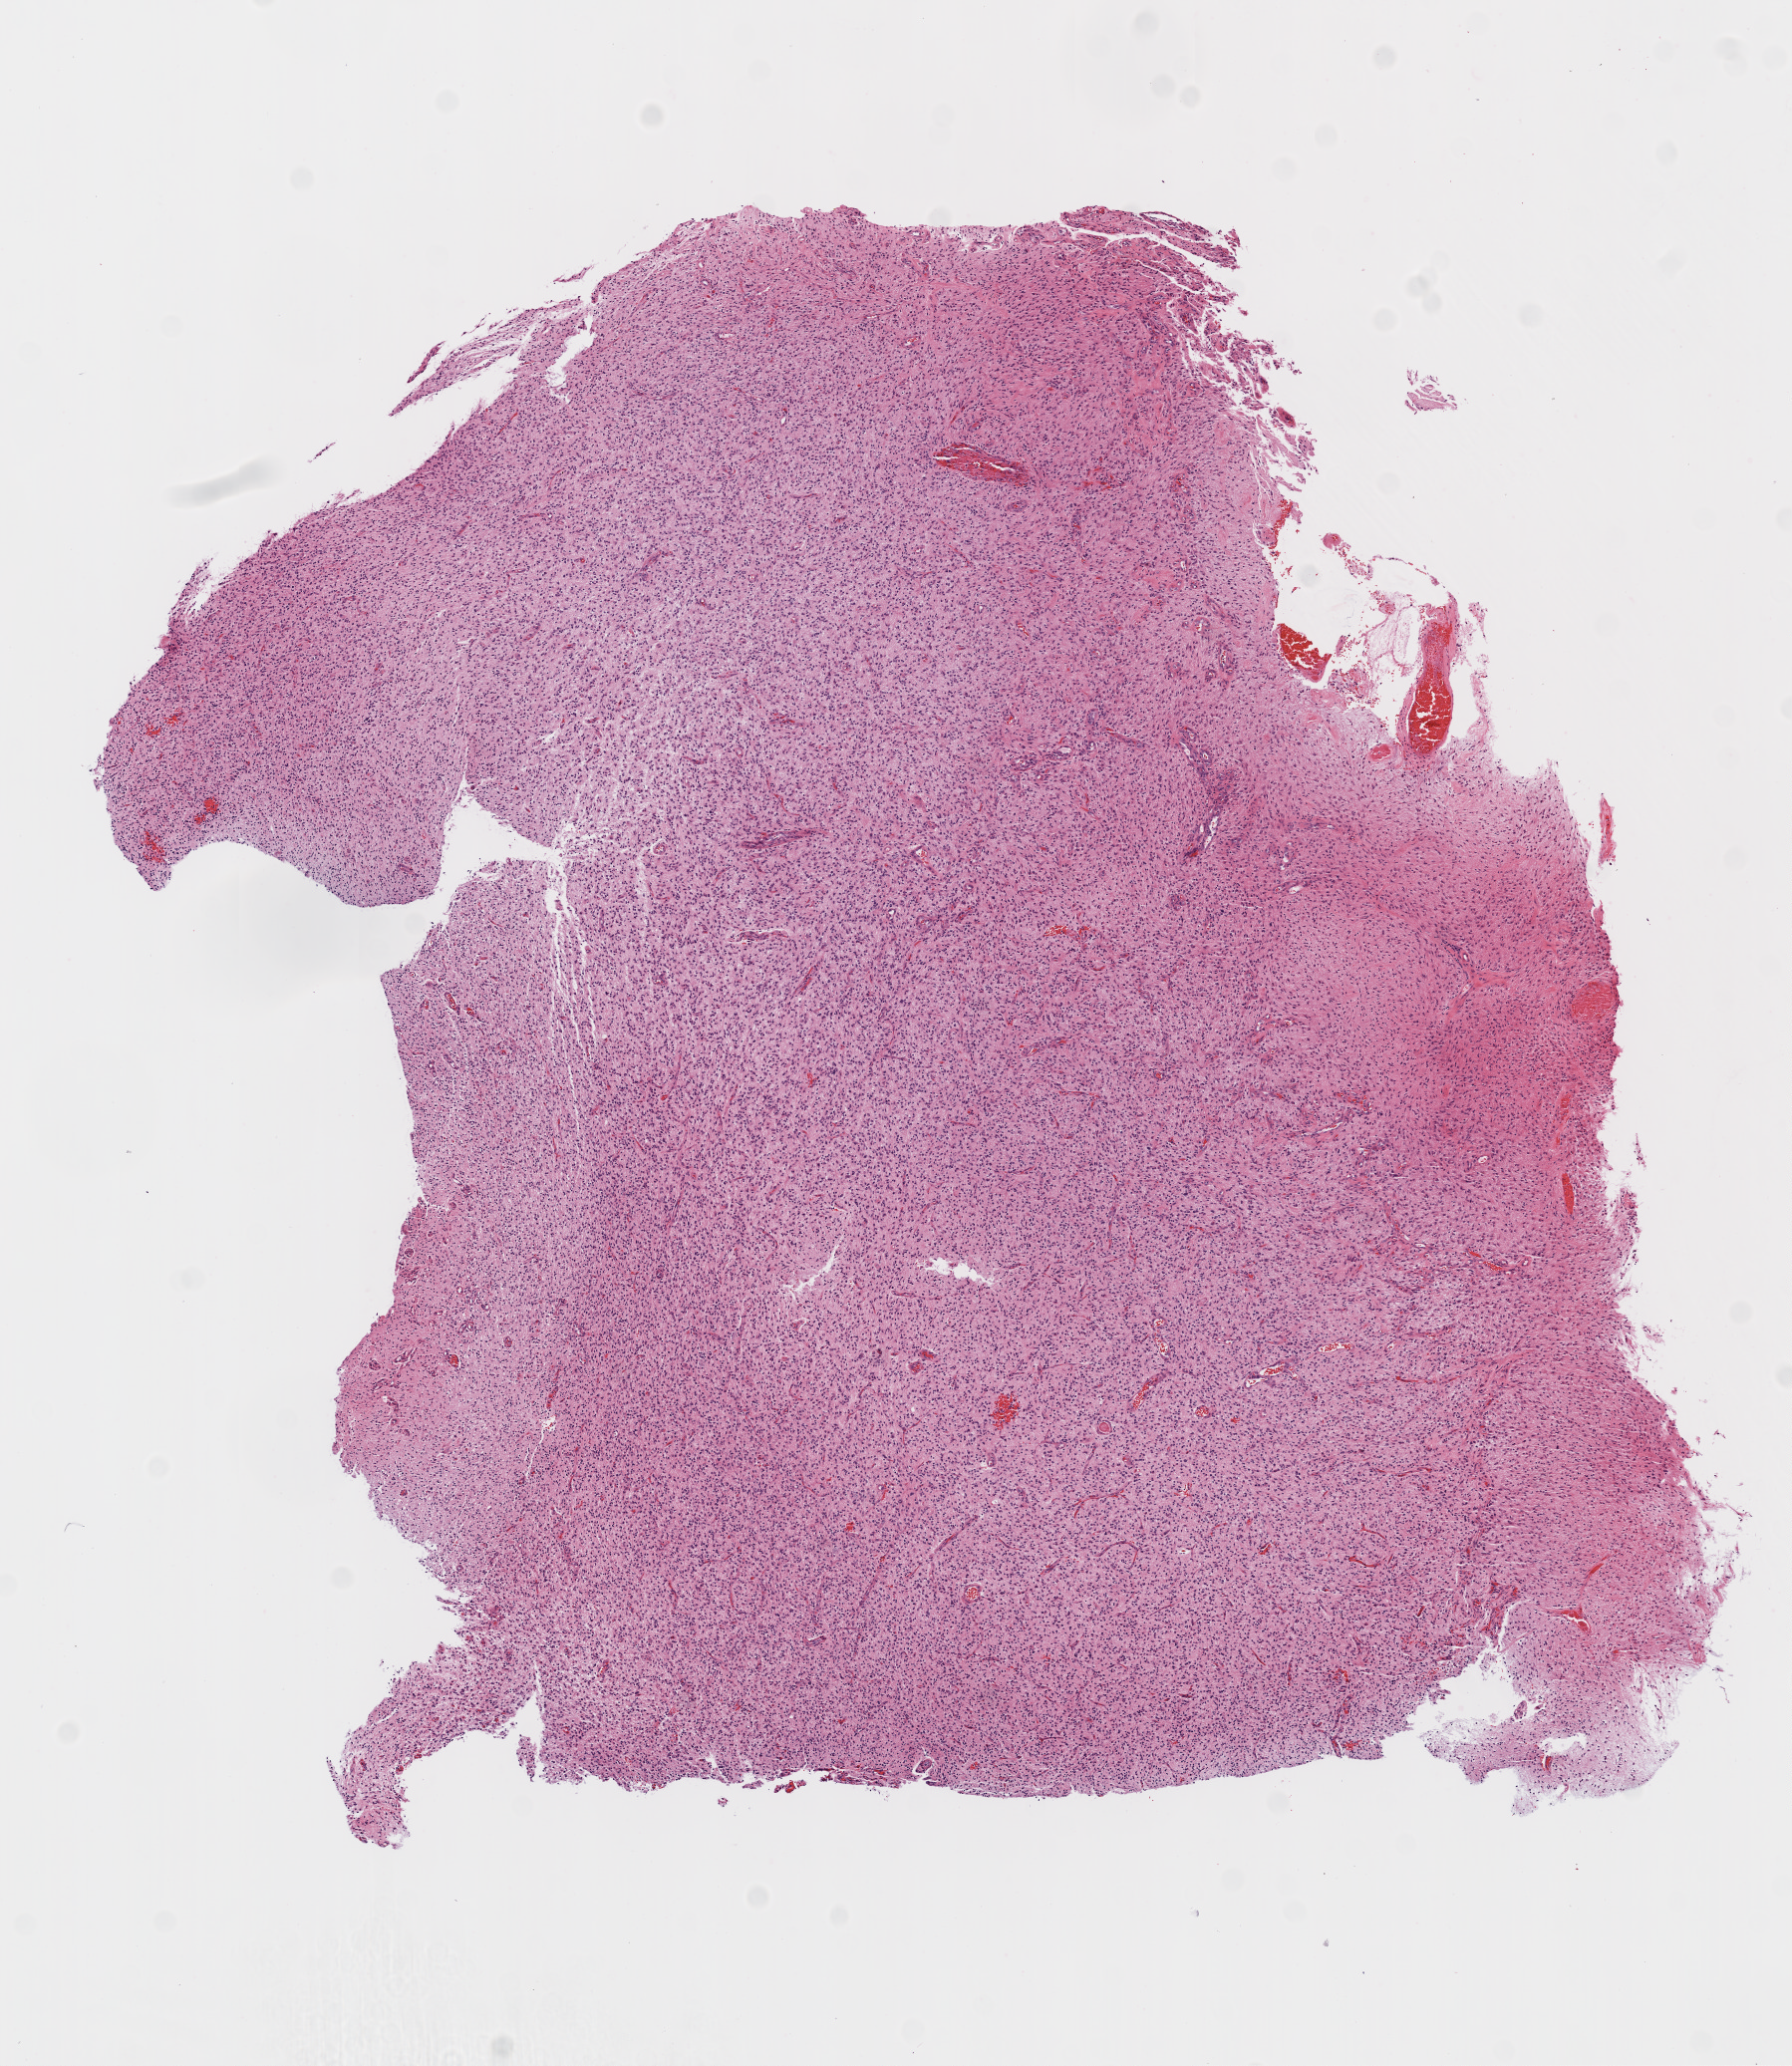
Digitized Hematoxylin and eosin (H&E) stained tissue section (whole slide), shown as a low-resolution overview of the whole scanned area (about 7.3 x 8.4 mm), FFPE section, sample: primary tumour, brain. Patient: male, age at initial diagnosis 86 years.
• diagnosis: Glioblastoma